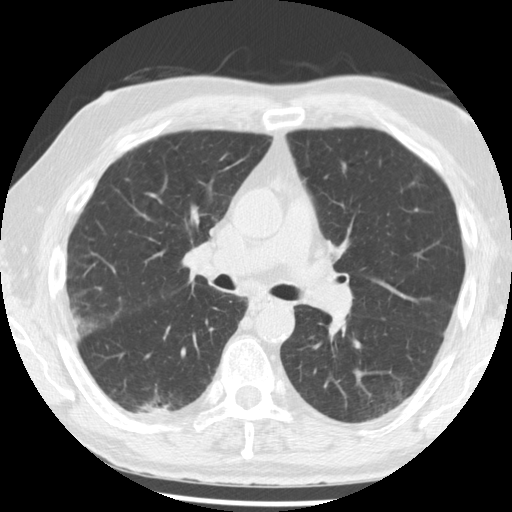
Low-dose screening chest CT, one axial slice. Position 122 of 221 along the scan axis. 120 kVp. Lung window (W 1500 / L -600 HU). 2.5 mm slice thickness. 512 × 512 image matrix.
Structures marked on this image (manually delineated by an expert):
- lesion 1 (tumor, lower lobe of right lung): box from (x=138, y=404) to (x=172, y=413) px